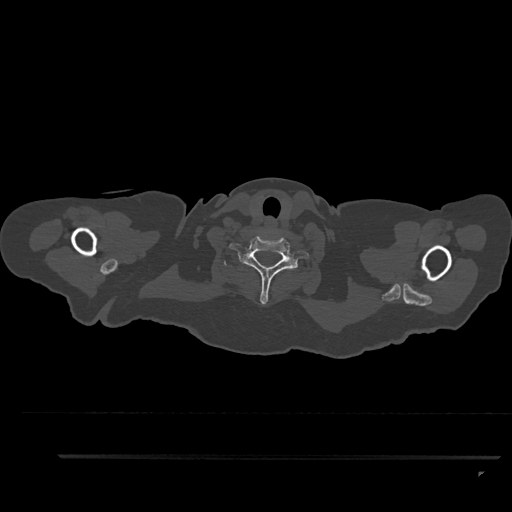
CT including the spine, one axial slice. Position 793 of 797 along the scan axis. Reconstruction kernel Br40s/3. Bone window (W 1800 / L 400 HU). 0.5 mm slice thickness. 512 × 512 image matrix. Patient: female, 44 years. Case-level facts recorded for this patient, not image findings: primary cancer: renal; vertebrae with lytic lesions (as recorded): L1.
Structures marked on this image (semi-automatic segmentation, software-assisted and operator-edited):
- T1 vertebra: bounding box <224,260,227,266> (left, top, right, bottom; pixels)